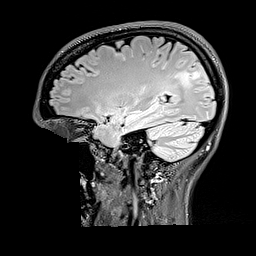
Brain MRI from a brain-tumour surgery series, one sagittal slice. Slice 114 of 176 in the series (ordered by position). T2 FLAIR. 1 mm slice thickness. 256 × 256 image matrix, field of view 256 × 256 mm. From the clinical record (not read from this slice): histopathology: Oligodendroglioma; WHO grade: 2; IDH mutation: yes.
Structures marked on this image (manually delineated by an expert):
- tumour: bounding box <172,84,174,89> (left, top, right, bottom; pixels)